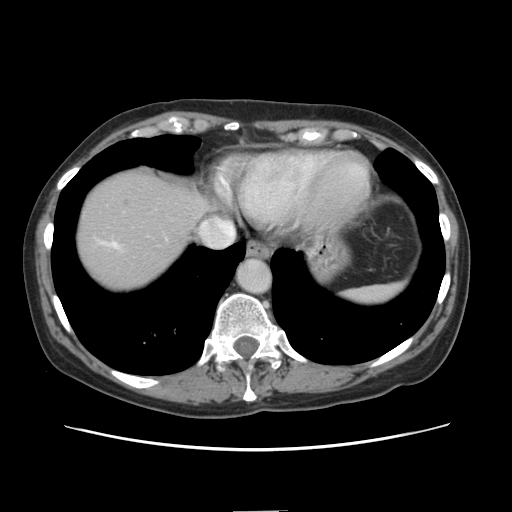
Contrast-enhanced abdominal CT, one axial slice; position 126 of 141 along the scan axis; 120 kVp; soft-tissue window (W 400 / L 40 HU); 2.5 mm slice thickness; 512 × 512 image matrix, field of view 350 × 350 mm. Female patient, age 63 years. From the clinical record (not read from this slice): diagnosis: colorectal cancer liver metastases, imaged before liver resection; multiple liver metastases: yes; largest metastasis: 3.2 cm; disease in both lobes: yes.
Annotated regions visible in this slice (outlined manually by an expert reader):
- hepatic veins: box from (x=110, y=242) to (x=118, y=247) px
- liver: (x=76, y=165)–(x=210, y=293)